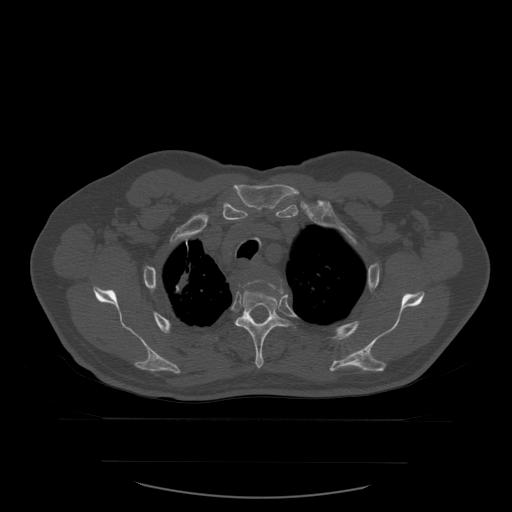
CT including the spine, one axial slice; slice 444 of 590 in the series (ordered by position); bone window (W 1800 / L 400 HU); 512 × 512 image matrix. Patient age 71 years. From the clinical record (not read from this slice): primary cancer: lung; vertebrae with lytic lesions (as recorded): T1, T2, L5, S1.
Annotated regions visible in this slice (semi-automatic segmentation, software-assisted and operator-edited):
- T3 vertebra: bounding box (x1, y1, x2, y2) in pixels: (243, 278, 283, 294)
- T4 vertebra: (235, 289, 290, 369)